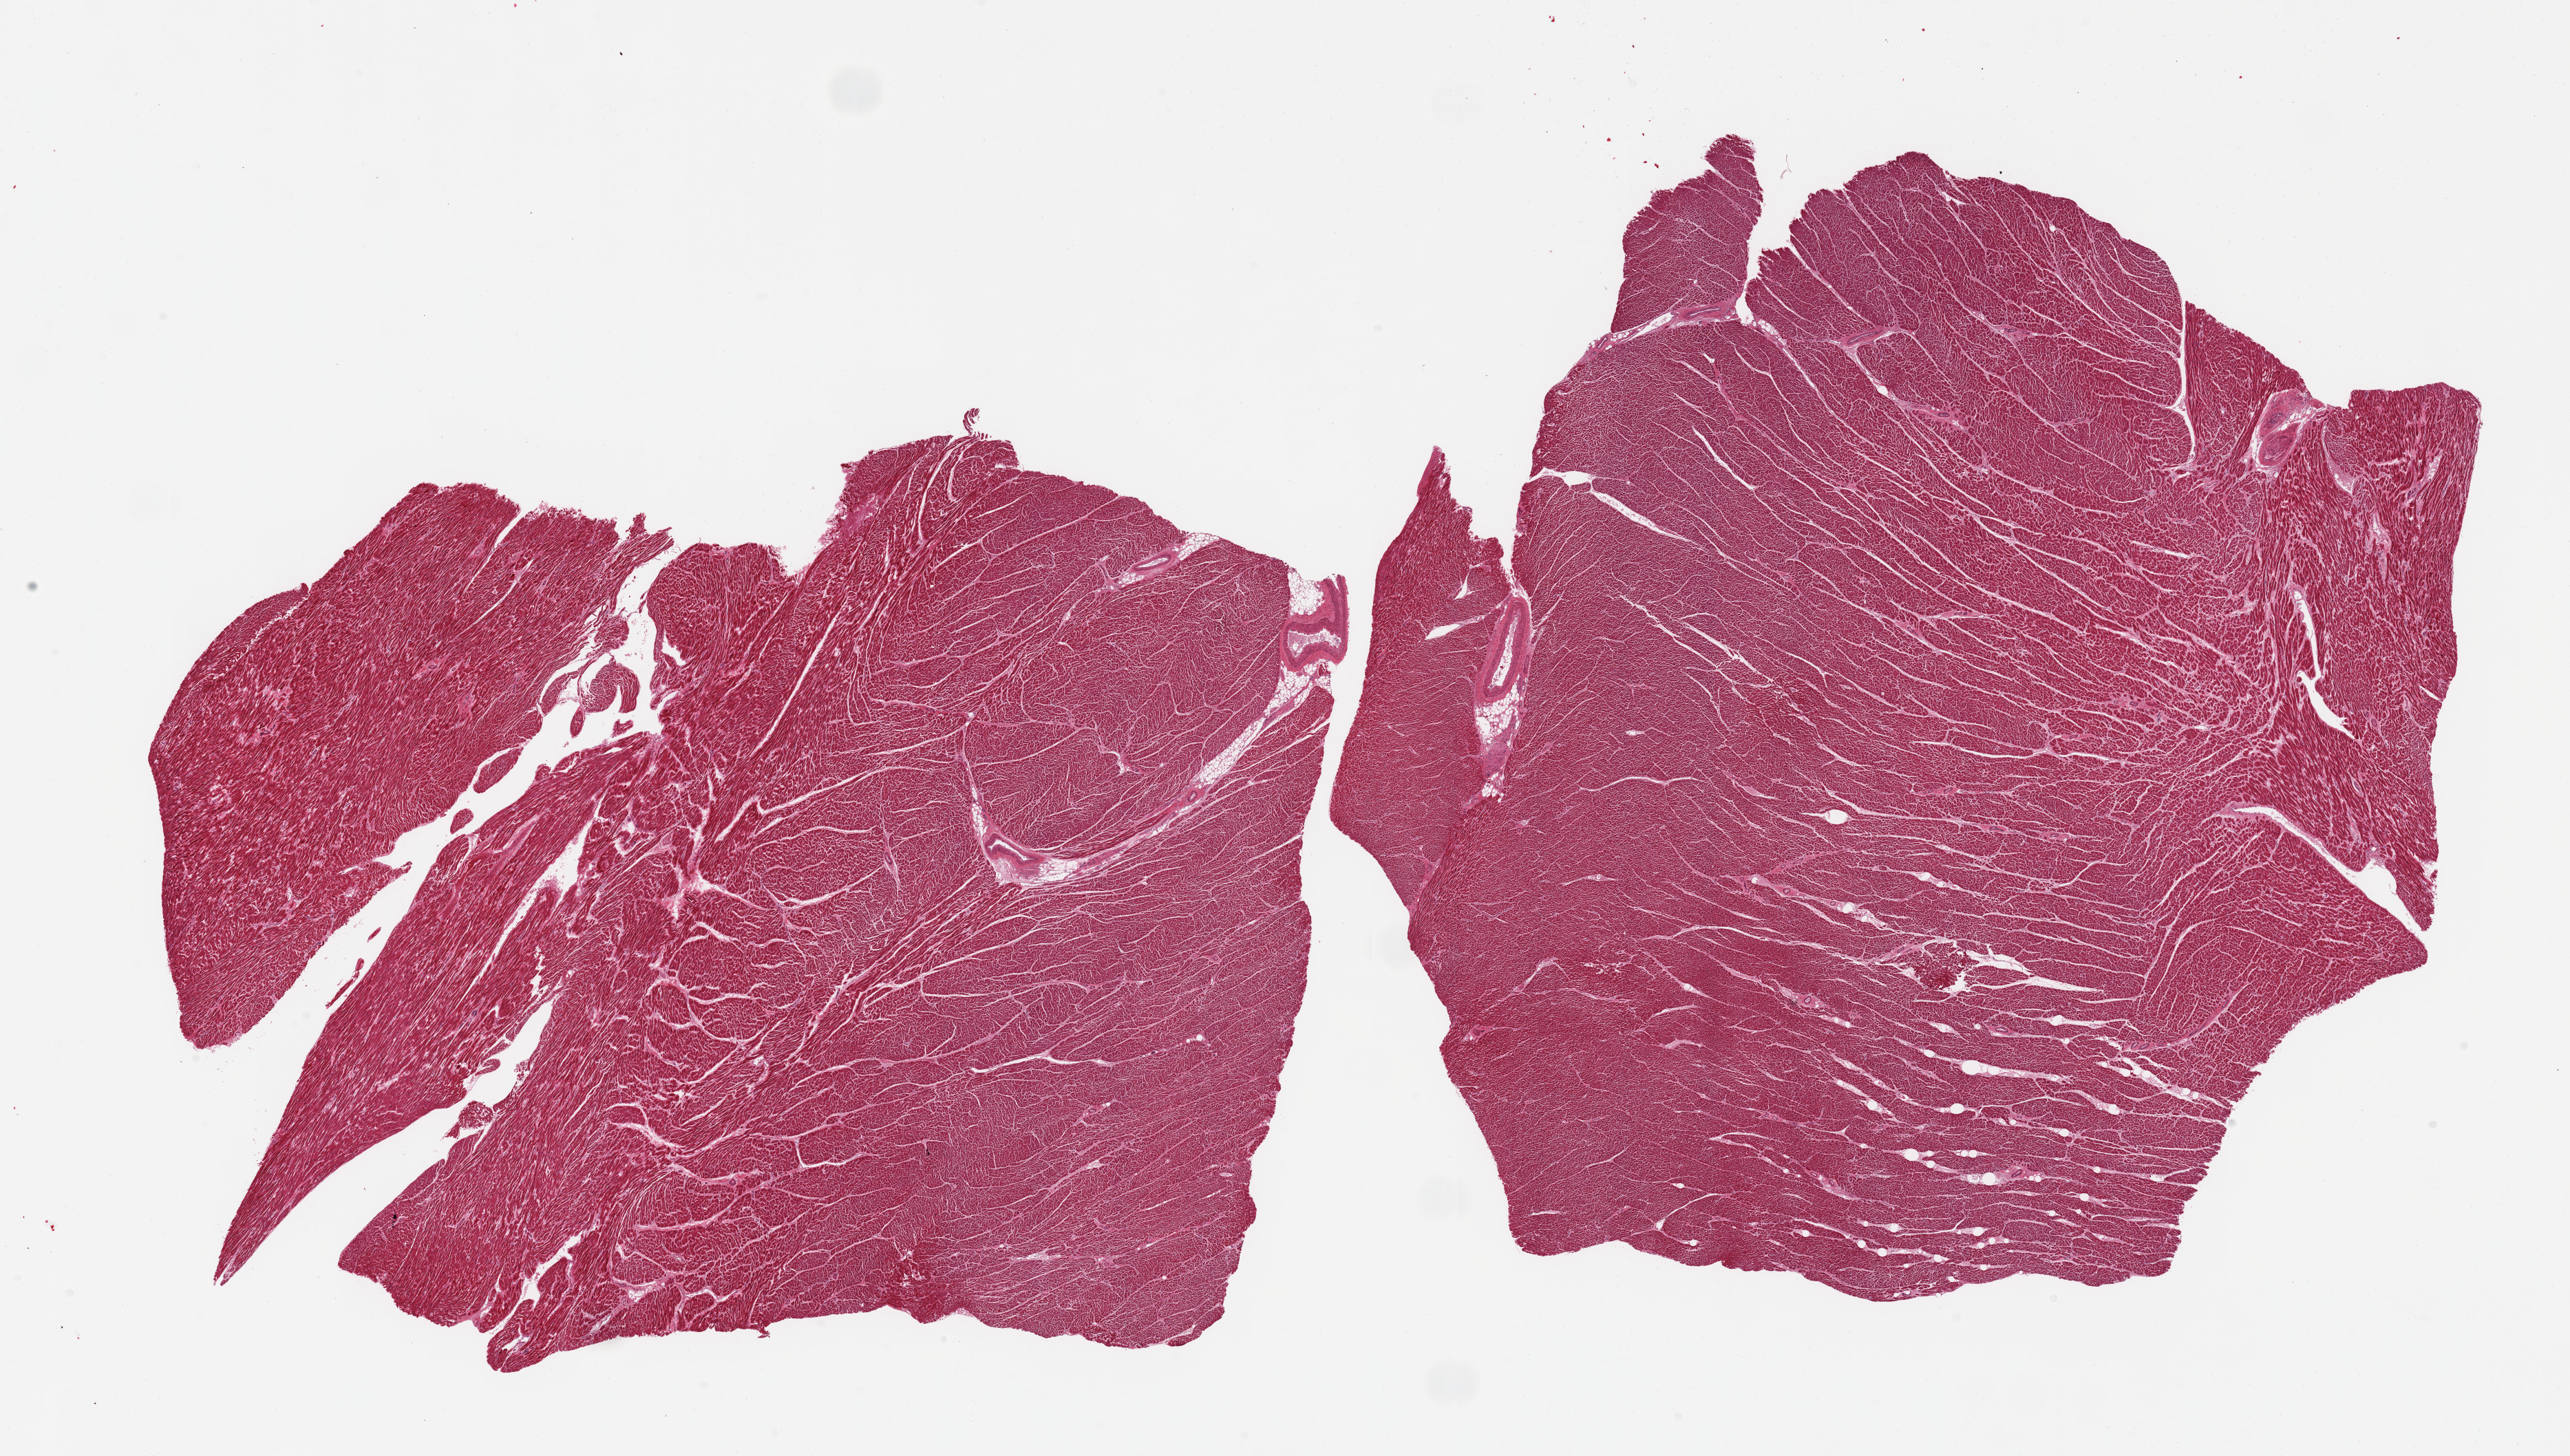
Digitized H&E-stained section, brightfield, a low-resolution overview of the entire scanned area, about 29.5 x 16.7 mm. PAXgene-fixed paraffin-embedded (PFPE) section. Sampled site (target tissue): heart. Donor tissue sample. Donor sex: female.
Review note (as recorded): 2 pieces; 2% internal fat.